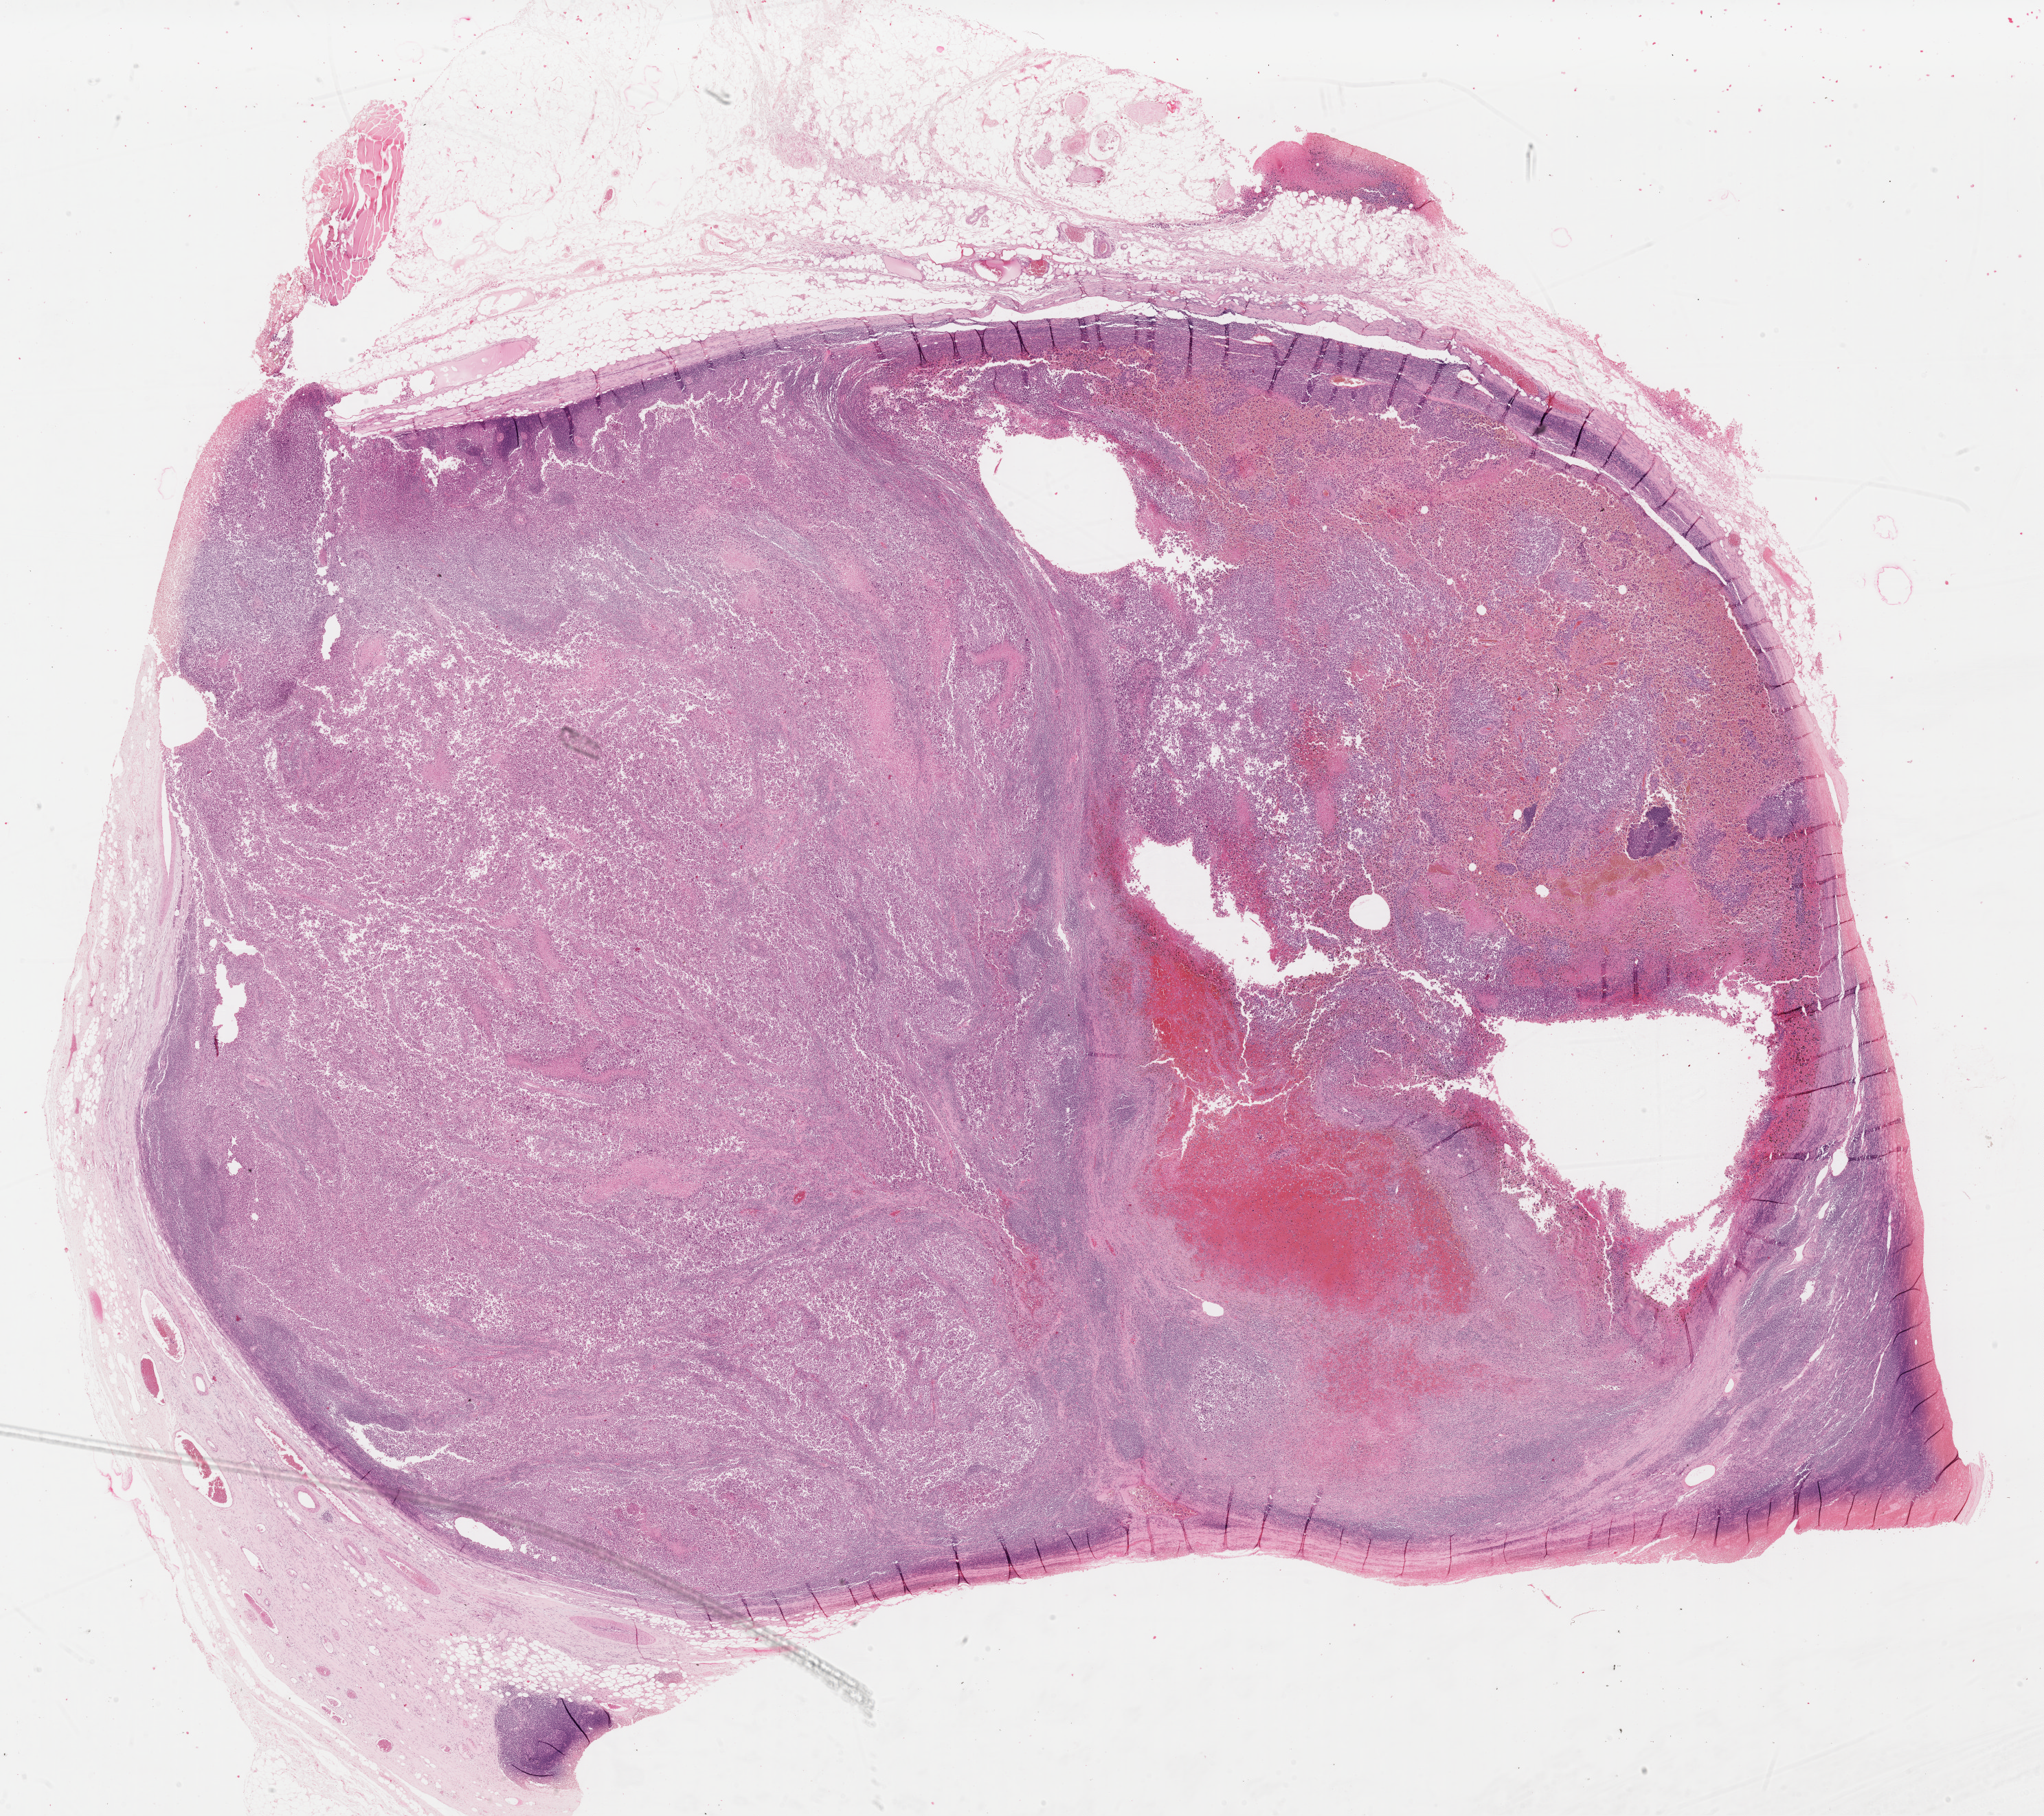
Whole-slide histology image, Hematoxylin and eosin (H&E) stained — shown as a low-resolution overview of the whole scanned area (about 23.5 x 20.9 mm); FFPE section; skin, primary tumour sample. Male, age 61 years at initial diagnosis.
Histologic diagnosis: Malignant melanoma, NOS.